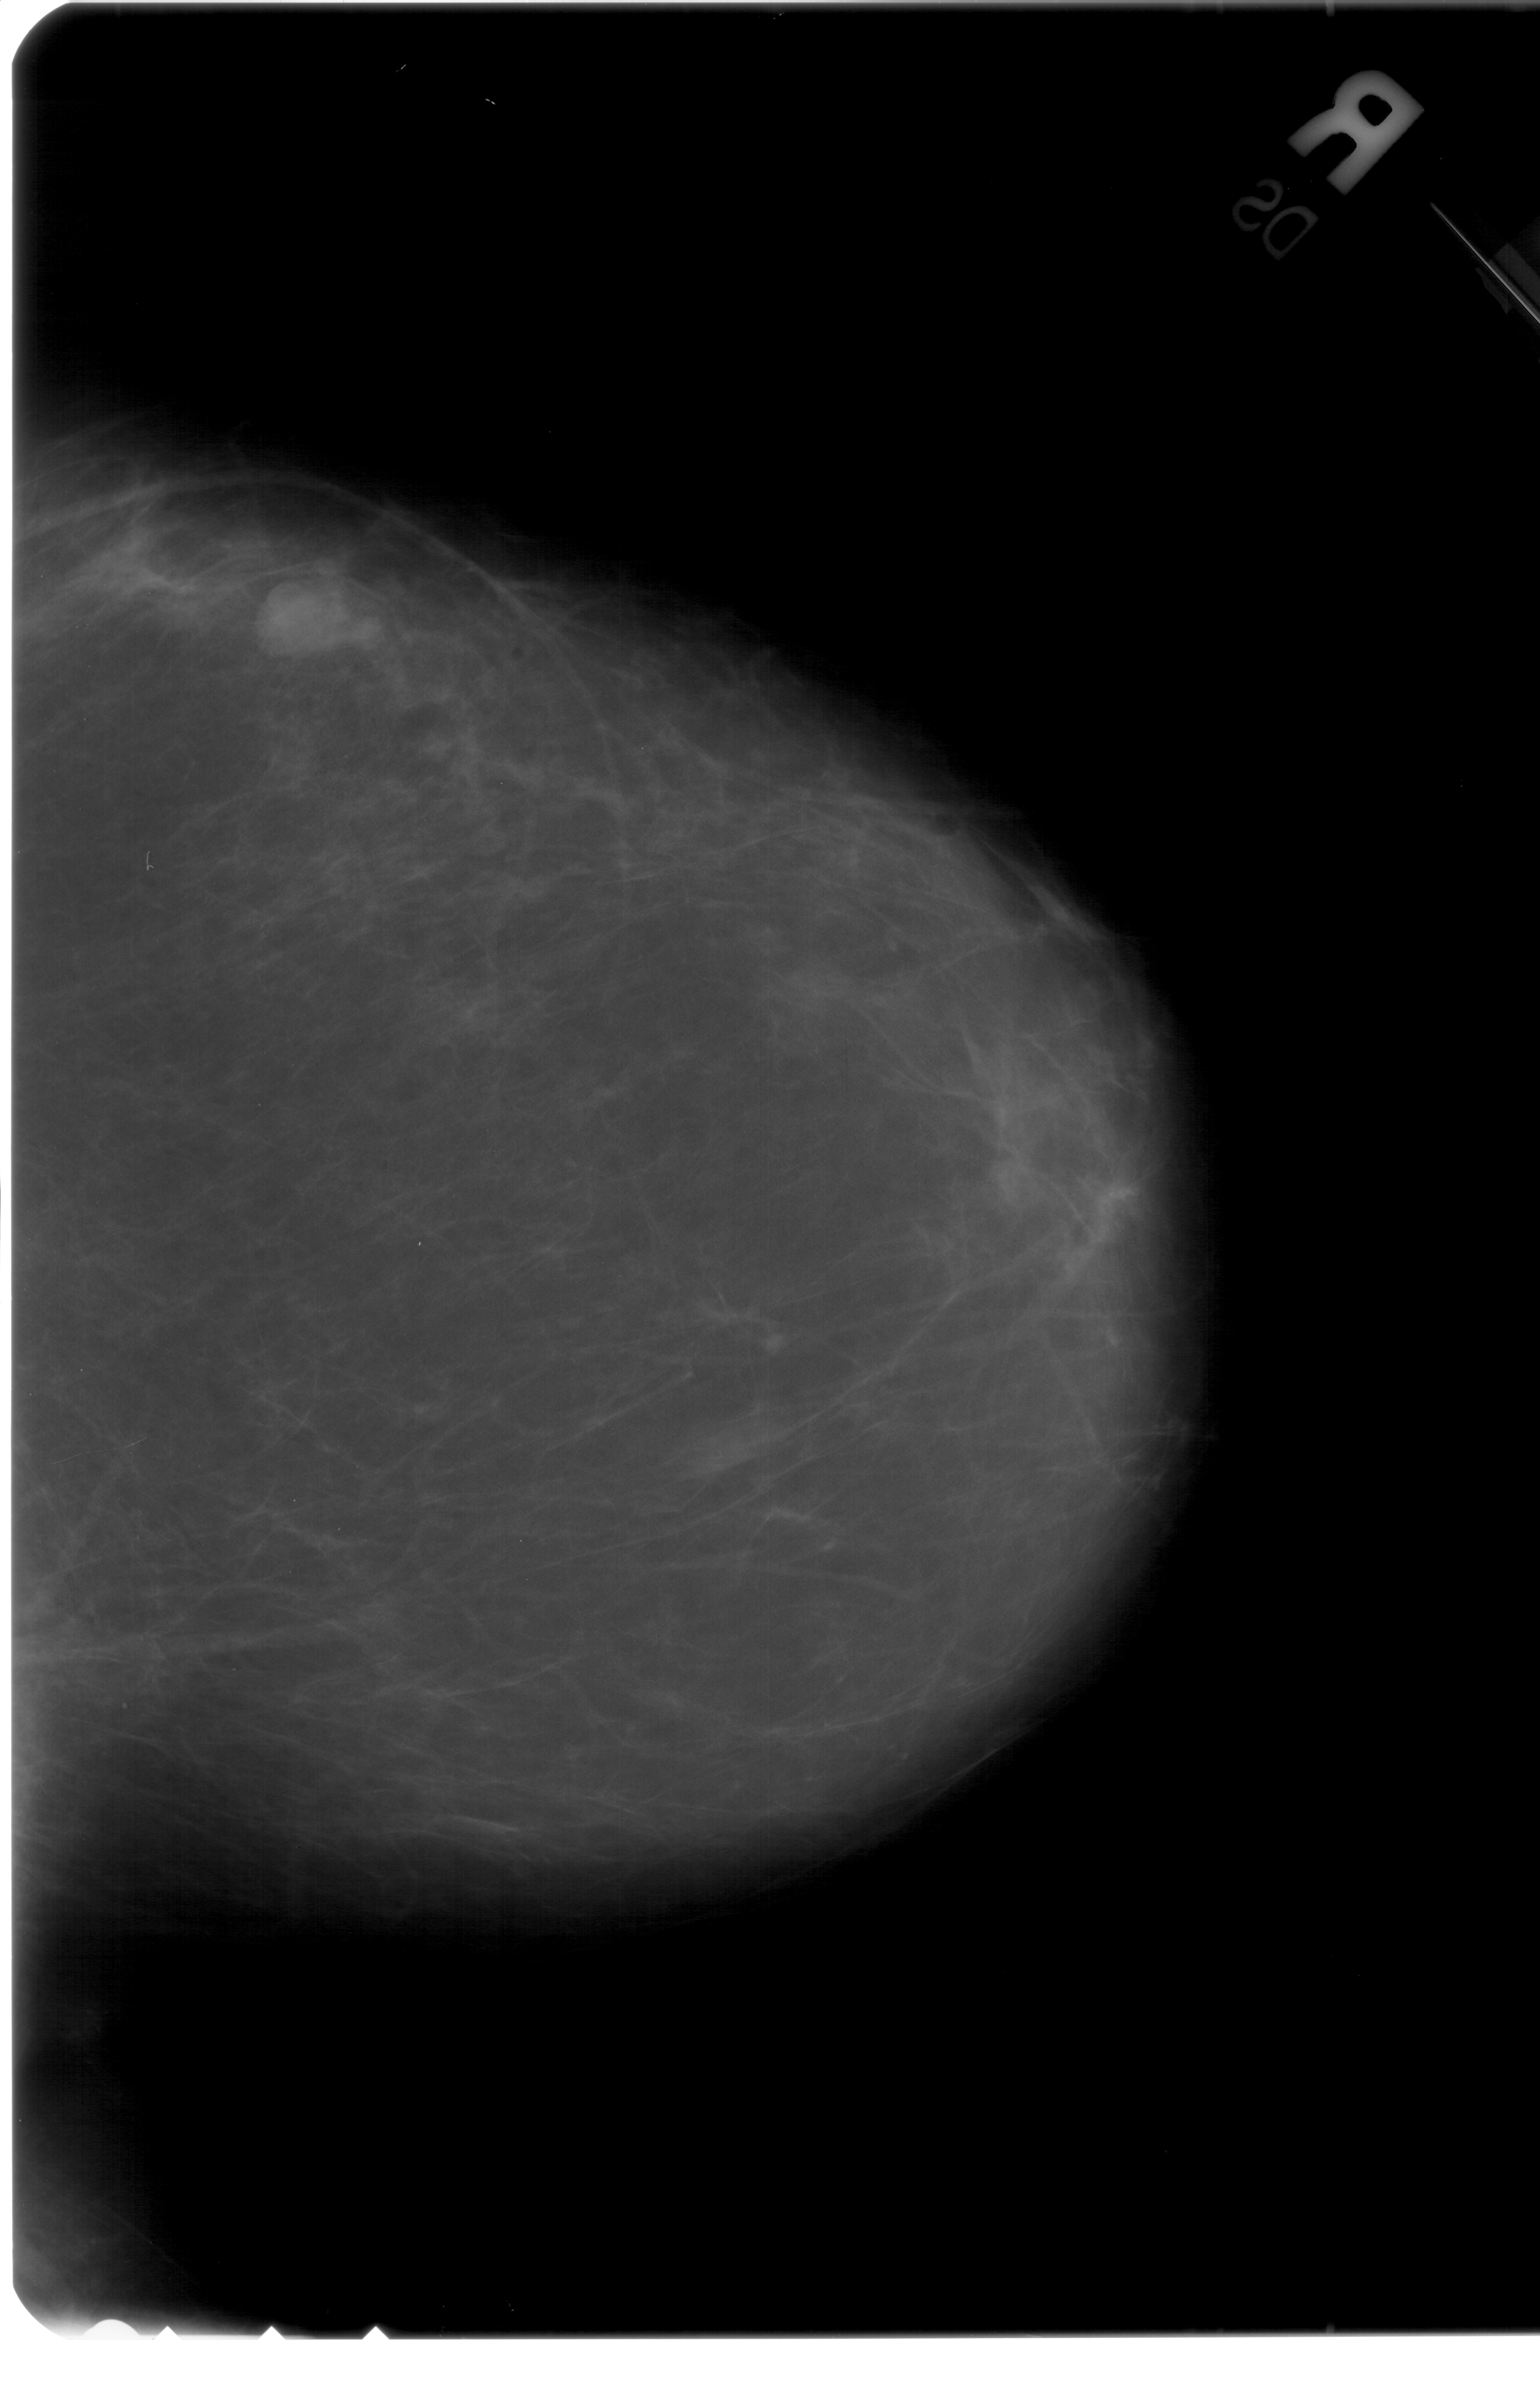
Digitized screen-film mammogram. Right breast. CC view. BI-RADS breast density category 2 (scale 1–4). 1540 × 2391 image matrix.
Expert-marked regions of interest on this film, with their recorded descriptors:
- mass, shape lobulated, margins circumscribed; BI-RADS assessment category 4; subtlety rating 4 on a 1 (subtle) to 5 (obvious) scale; pathology result (as recorded, not read from the image): benign: bounding box <248,562,390,683> (left, top, right, bottom; pixels)